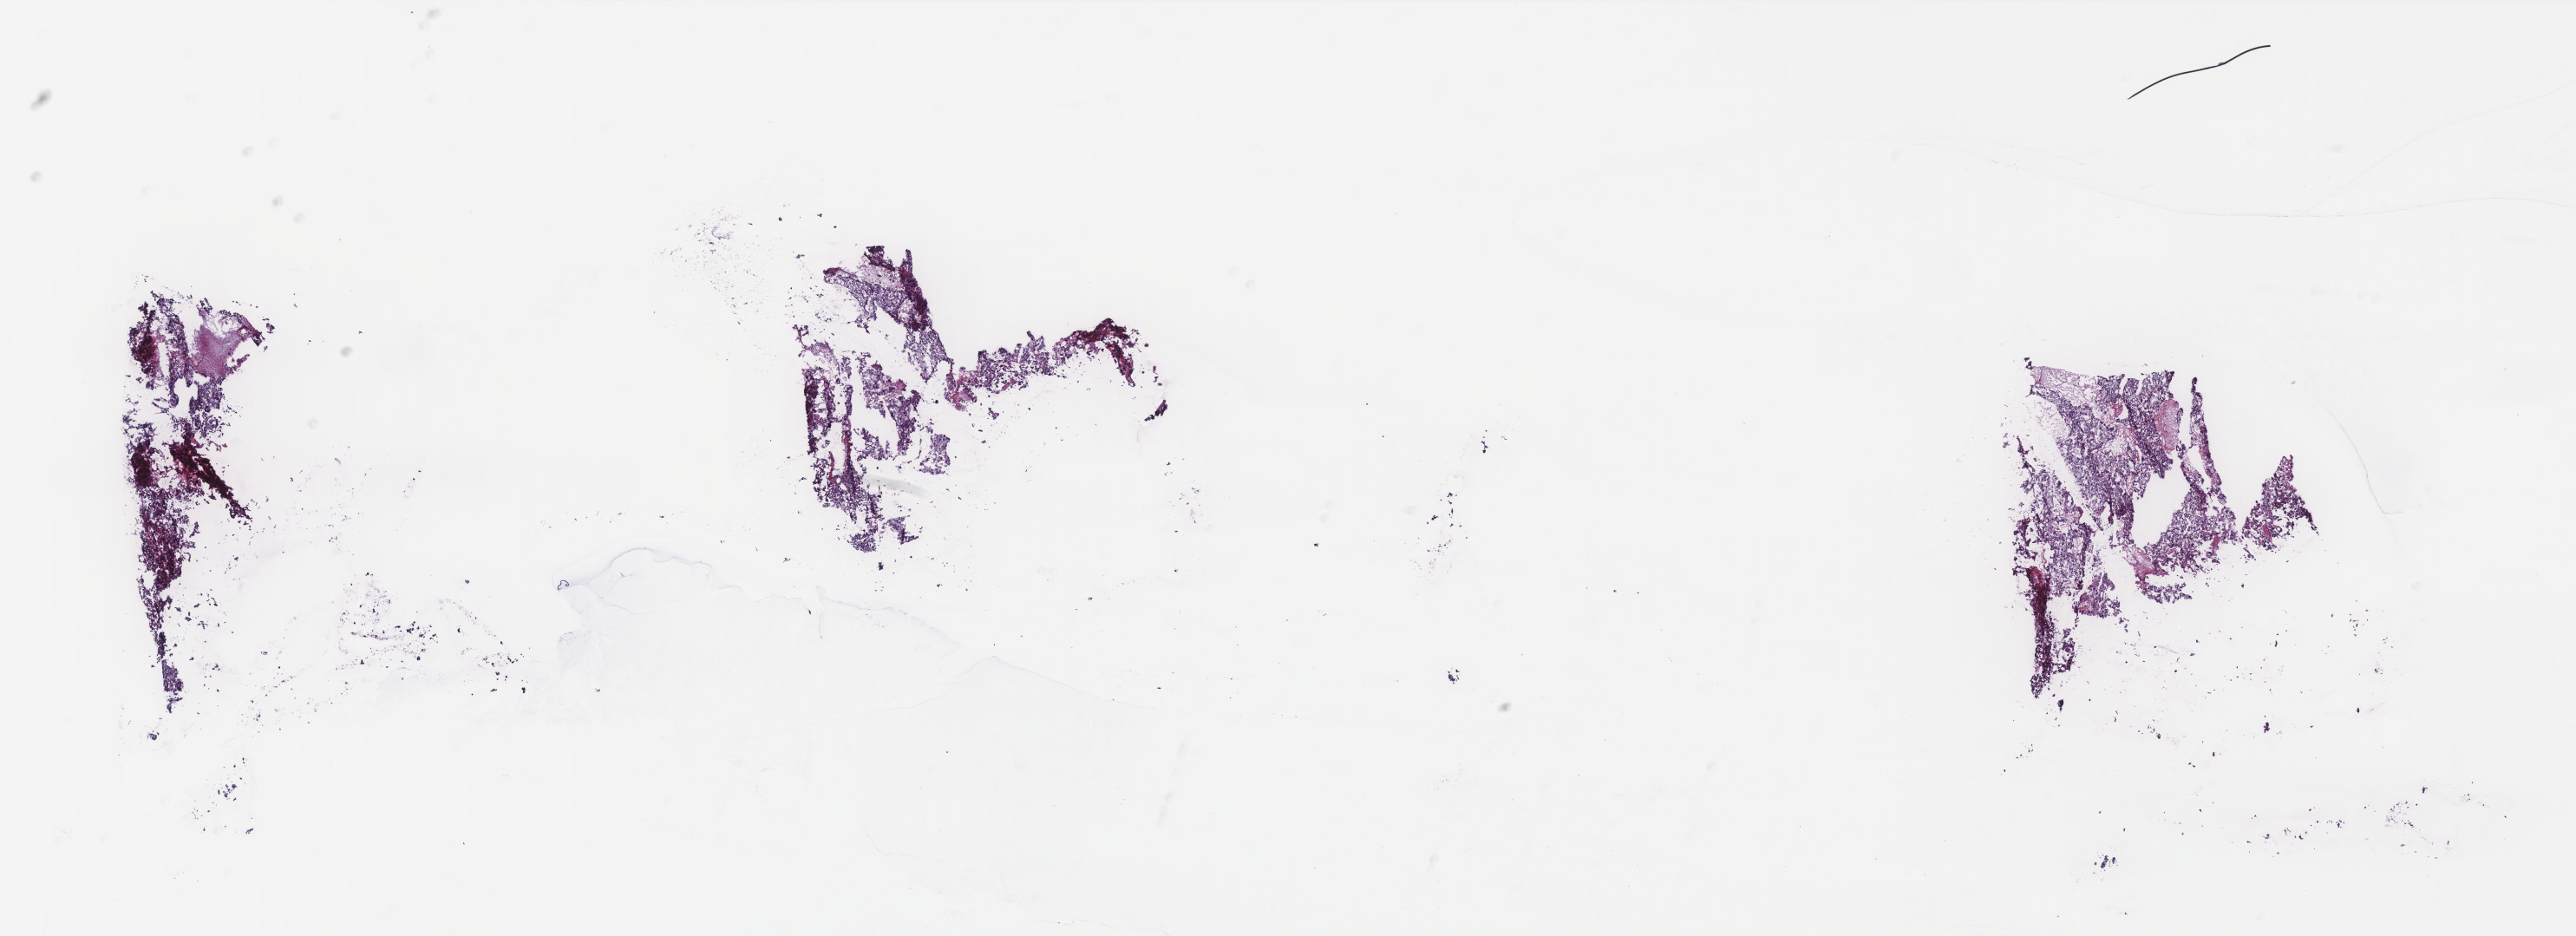
Digitized Hematoxylin and eosin (H&E) stained tissue section (whole slide) — low-resolution overview of the scanned area, about 23.8 x 8.7 mm. Frozen section from the top of the tissue portion. Sample: primary tumour, liver. Female patient; age at initial diagnosis 64 years. Histologic grade: G2 (moderately differentiated). Slide review estimates, as recorded: tumour cells 75%, tumour nuclei 80%, normal cells 0%, stromal cells 20%, necrosis 5%. Inflammatory infiltration, as recorded: lymphocyte infiltration 5%, monocyte infiltration 0%, neutrophil infiltration 0%.
Pathologic diagnosis: Hepatocellular carcinoma, NOS. TNM: T4 N0 M1. AJCC pathologic stage: IVB.